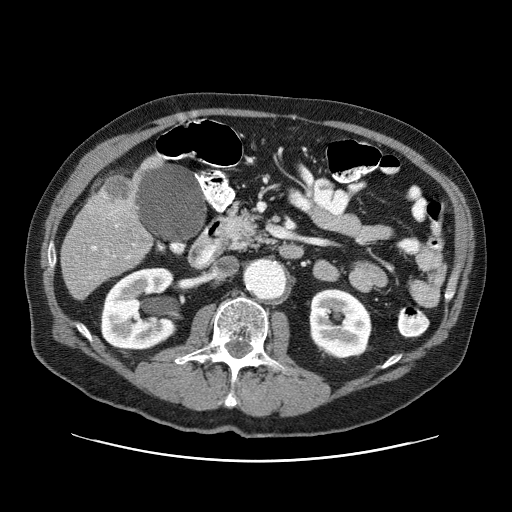
Contrast-enhanced abdominal CT (liver protocol), one axial slice. Slice 19 of 87 in the series (ordered by position). Reconstruction kernel STANDARD. 120 kVp. One of 3 acquisitions stored at this slice position. Soft-tissue window (W 400 / L 40 HU). 512 × 512 image matrix. Case-level facts recorded for this patient, not image findings: diagnosis: hepatocellular carcinoma (patient treated with transarterial chemoembolisation; whether this scan precedes or follows treatment is not stated here); TNM stage (as recorded): Stage-IIIA; Child-Pugh class: A; tumour differentiation: well differentiated; tumour nodularity: multinodular.
Structures marked on this image (semi-automatically segmented with operator editing):
- liver parenchyma outside the tumour (the mass and vessels are separate outlines, so this box may not span the whole liver): box from (x=60, y=154) to (x=162, y=300) px
- mass: (x=100, y=174)–(x=138, y=214)
- liver vessels: (x=92, y=225)–(x=134, y=258)